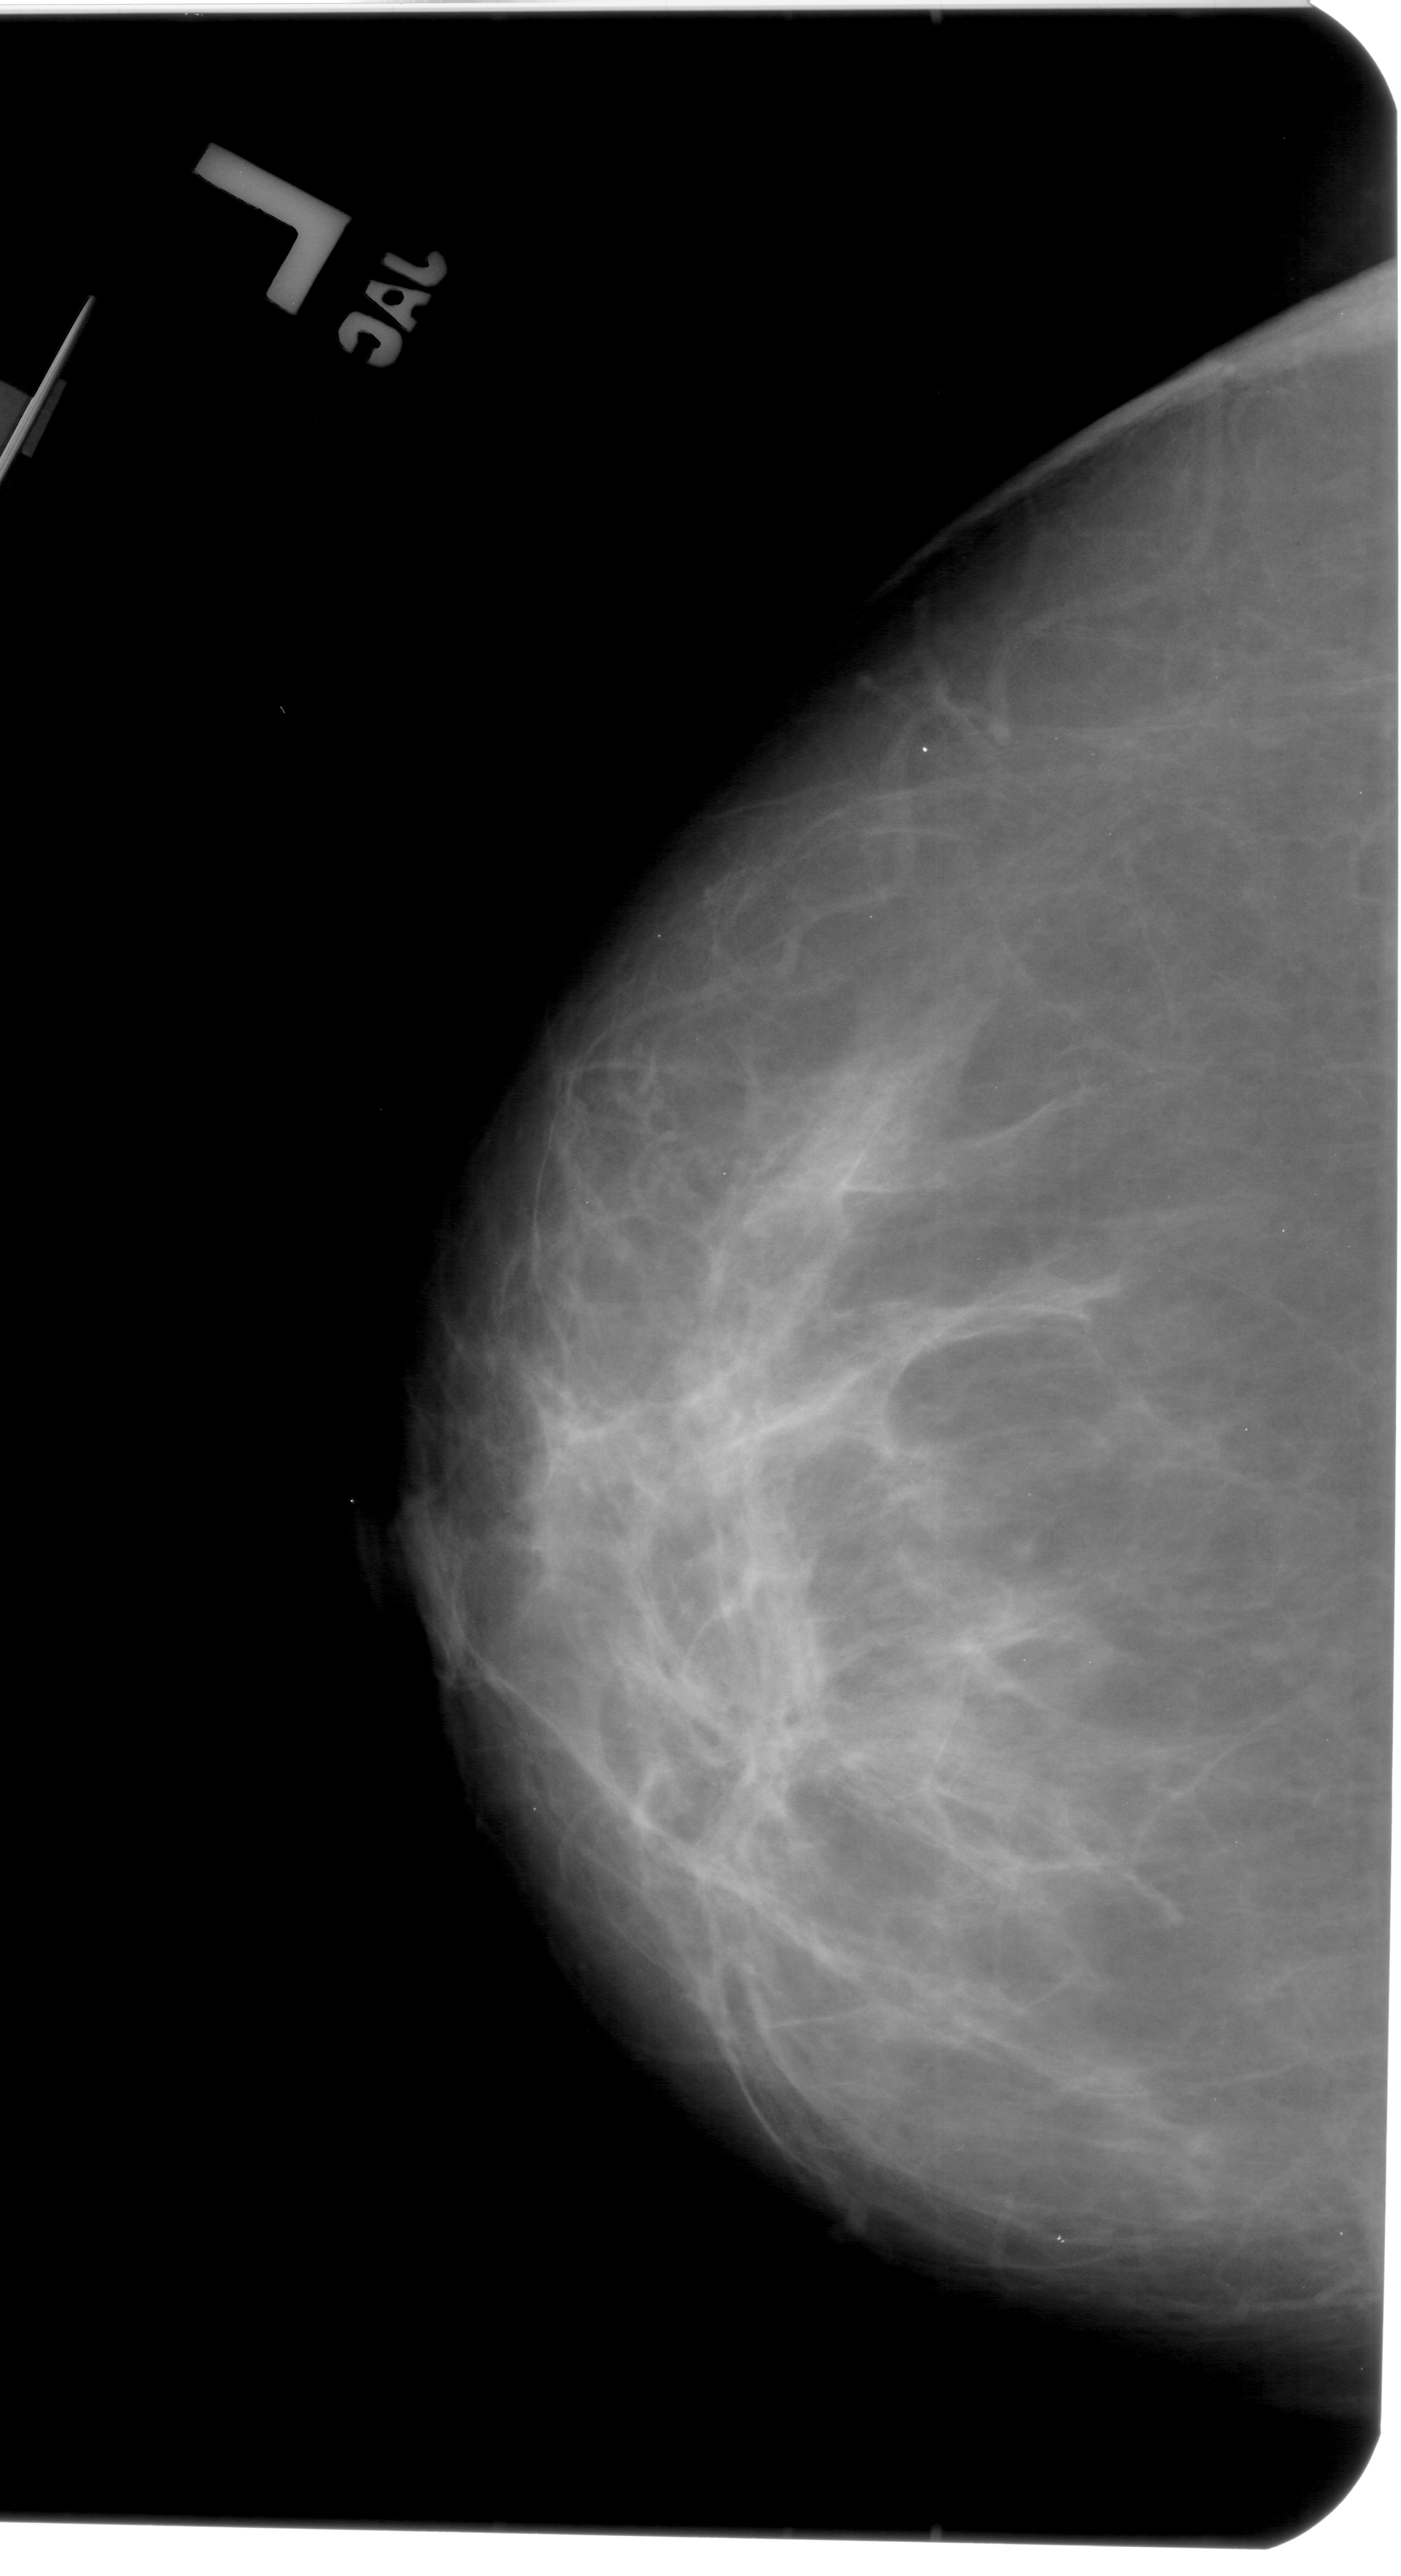
Digitized screen-film mammogram; left breast; craniocaudal (CC) view; BI-RADS breast density category 3 (scale 1–4).
- Radiologist-marked abnormalities on this image: mass, shape architectural distortion, margins ill defined; BI-RADS assessment category 4; pathology result (as recorded, not read from the image): benign.